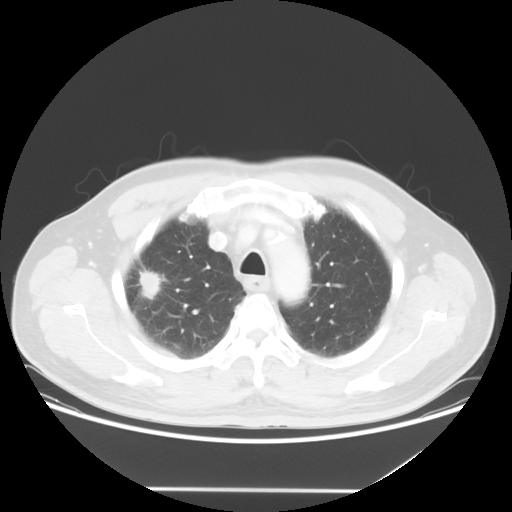
Chest CT, one axial slice. Position 42 of 54 along the scan axis. Reconstruction kernel STANDARD. 120 kVp. Lung window (W 1500 / L -600 HU). 512 × 512 image matrix, field of view 416 × 416 mm. Male patient, age 65 years. From the clinical record (not read from this slice): clinical TNM (as recorded): T1c N1 M0.
Outlined on this slice (rectangle marked by the reading radiologist):
- lung tumour (recorded histology: adenocarcinoma): bounding box (x1, y1, x2, y2) in pixels: (130, 266, 164, 306)